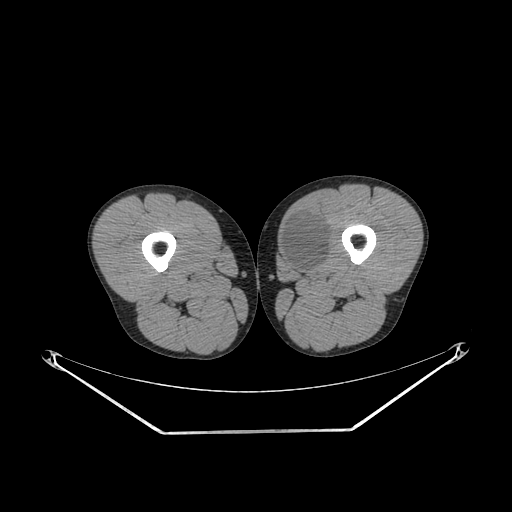
CT of an extremity soft-tissue mass (from a PET/CT study), one axial slice; slice 247 of 311 in the series (ordered by position); reconstruction kernel SOFT; 140 kVp; soft-tissue window (W 400 / L 40 HU); 3.75 mm slice thickness; 512 × 512 image matrix, field of view 500 × 500 mm. Male patient. From the clinical record (not read from this slice): histological type: mixoid liposarcoma; grade: low; site of the primary tumour: left thigh.
Outlined on this slice (expert contour drawn on MRI and transferred to this co-registered scan by the dataset authors):
- gross tumour volume (mass): bounding box [x1, y1, x2, y2] px = [281, 215, 330, 273]